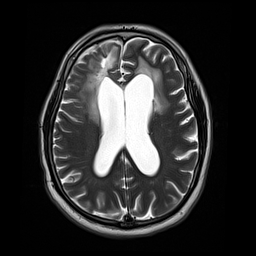
Brain MRI from a brain-tumour surgery series, one axial slice. Slice 18 of 44 in the series (ordered by position). 4 mm slice thickness. 256 × 256 image matrix, field of view 240 × 240 mm. Case-level facts recorded for this patient, not image findings: histopathology: Astrocytoma; WHO grade: 4; IDH mutation: yes; tumour location: Right Frontal.
Structures marked on this image (manually delineated by an expert):
- tumour: bounding box <88,98,101,125> (left, top, right, bottom; pixels)